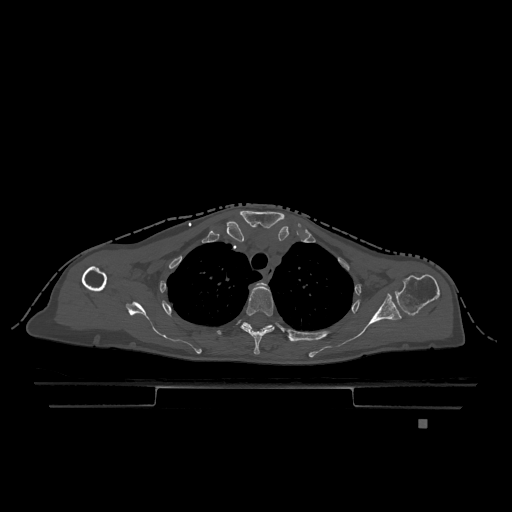
CT including the spine, one axial slice; slice 915 of 1317 in the series (ordered by position); bone window (W 1800 / L 400 HU); 0.5 mm slice thickness; 512 × 512 image matrix, field of view 500 × 500 mm. Patient: female, 74 years. From the clinical record (not read from this slice): primary cancer: lung; vertebrae with lytic lesions (as recorded): T1, T4, T5, T6, L4, L5.
Outlined on this slice (semi-automatically segmented with operator editing):
- T2 vertebra: bounding box [x1, y1, x2, y2] px = [252, 282, 266, 291]
- T3 vertebra: [241, 286, 275, 355]
- T4 vertebra: [243, 322, 307, 342]